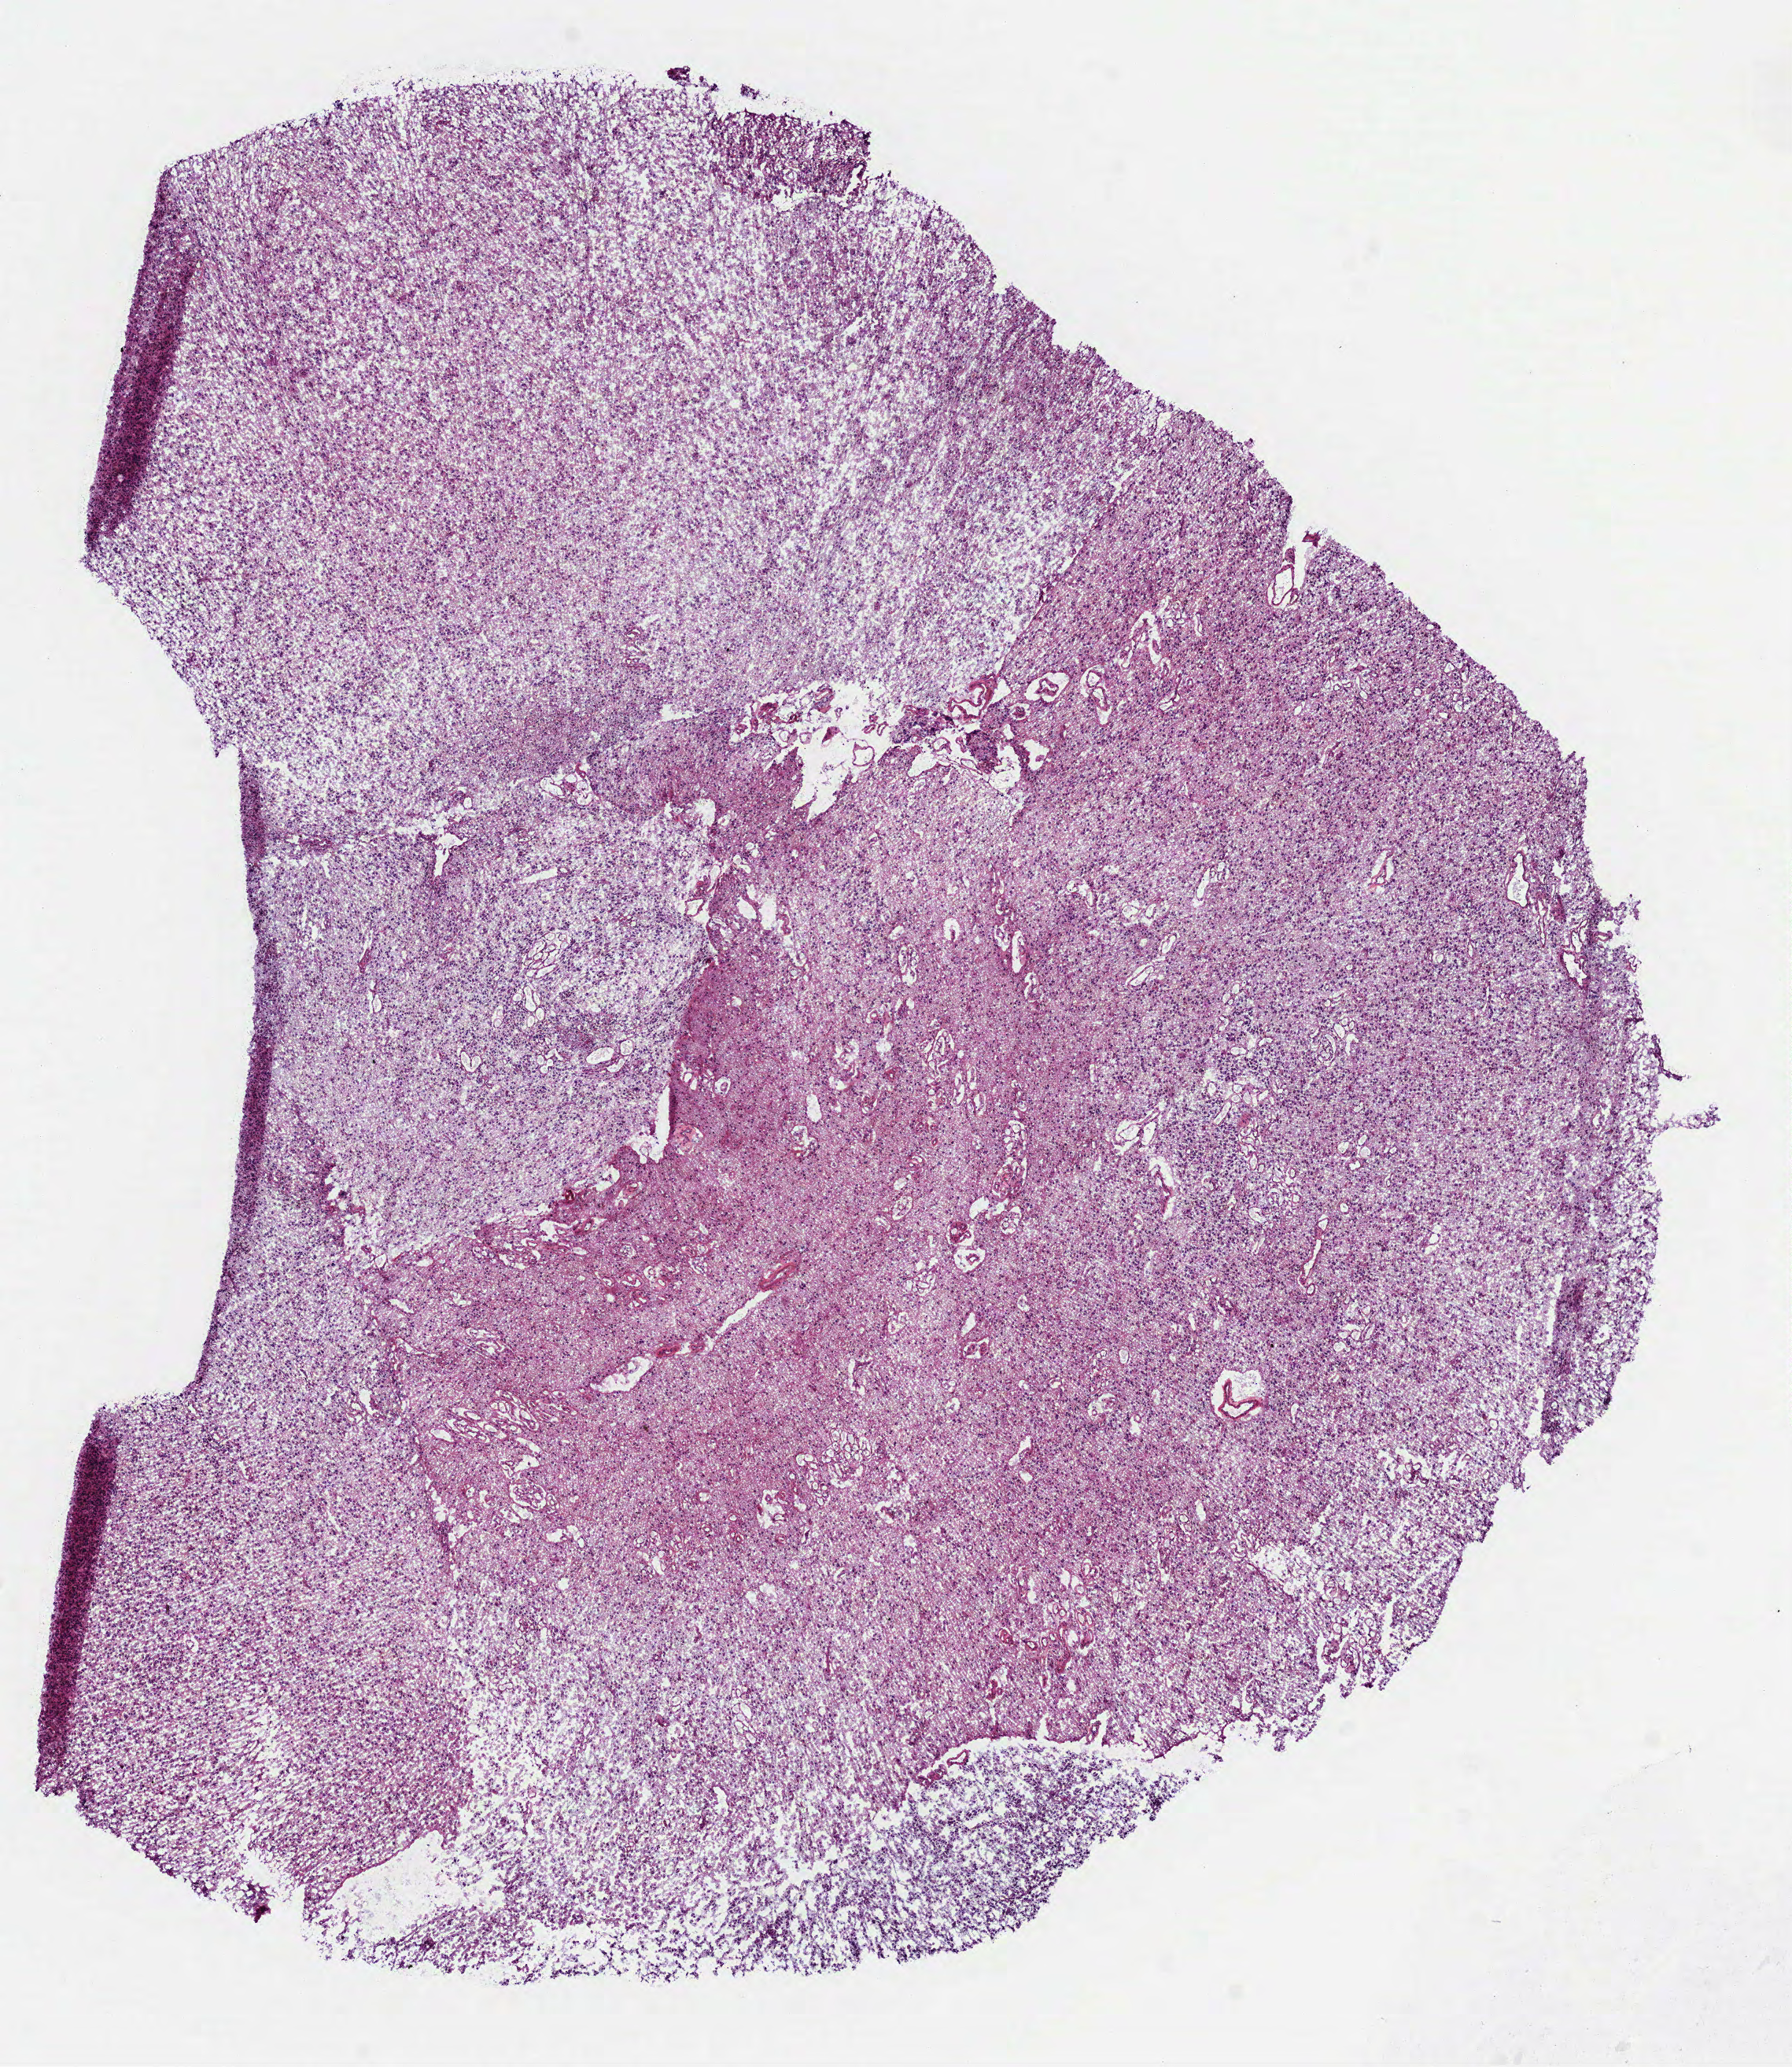
Hematoxylin and eosin (H&E) stained whole-slide image — low-resolution overview of the scanned area, about 9.2 x 10.6 mm (acquisition: 40x scan), frozen section from the top of the tissue portion, primary tumour sample from the brain. Patient: male, age at initial diagnosis 59 years. Histologic grade: G2 (moderately differentiated). Composition of this section per pathologist review: tumour cells 100%, tumour nuclei 80%, normal cells 0%, stromal cells 0%, necrosis 0%.
• diagnosis: Oligodendroglioma, NOS (cerebrum)